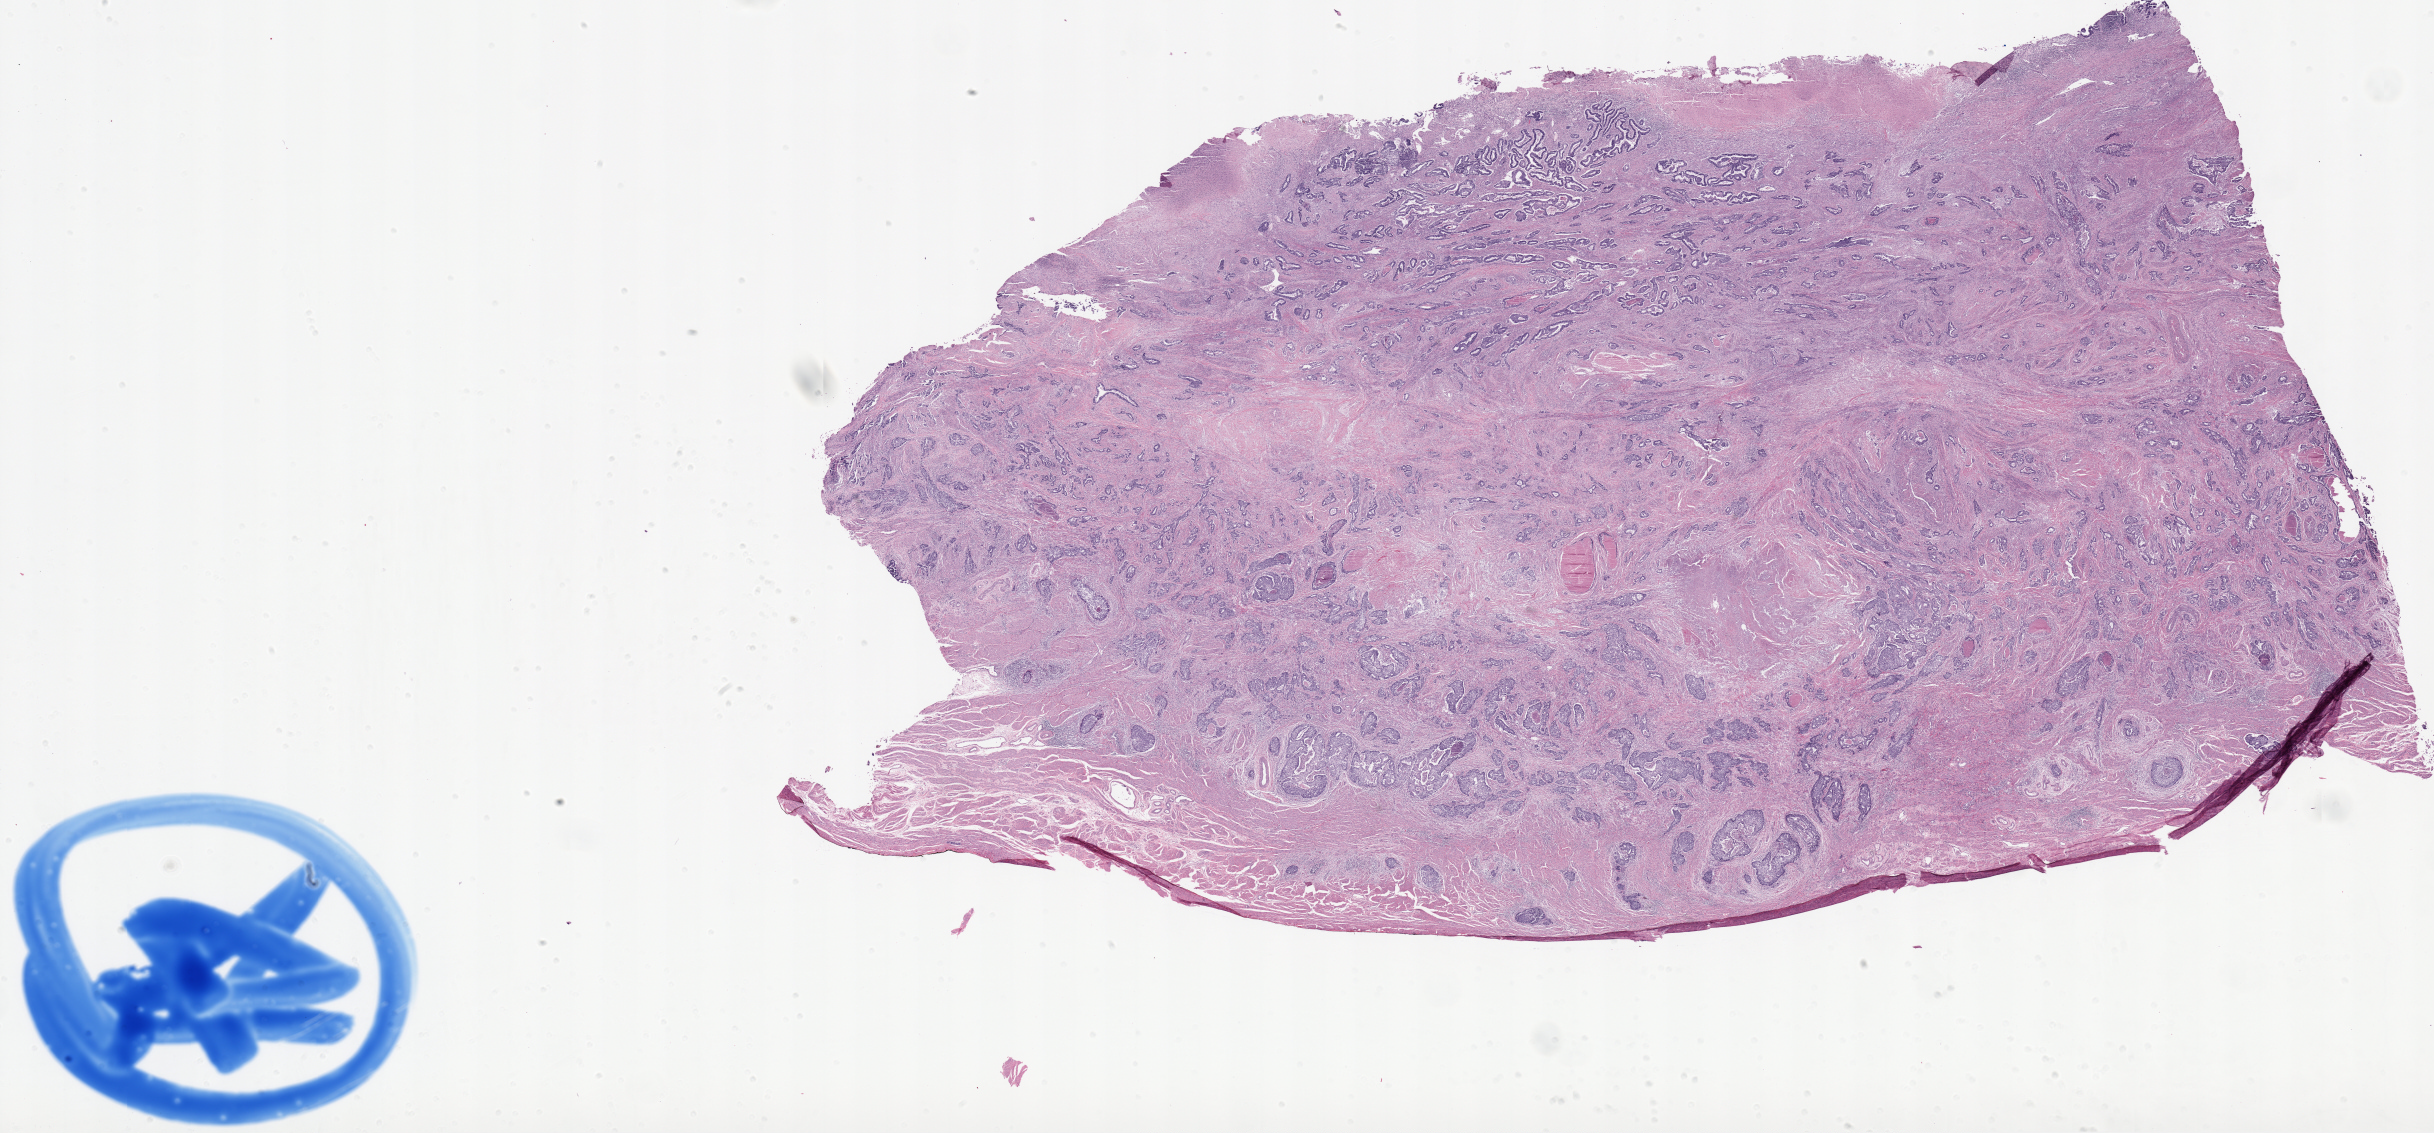
Digitized H&E-stained tissue section (whole slide) — whole scanned area (about 38.8 x 18.1 mm) shown as a low-resolution overview; FFPE section; sample: primary tumour, uterus. Female, age 64 years at initial diagnosis.
Pathologic diagnosis: Endometrioid adenocarcinoma, NOS (endometrium).